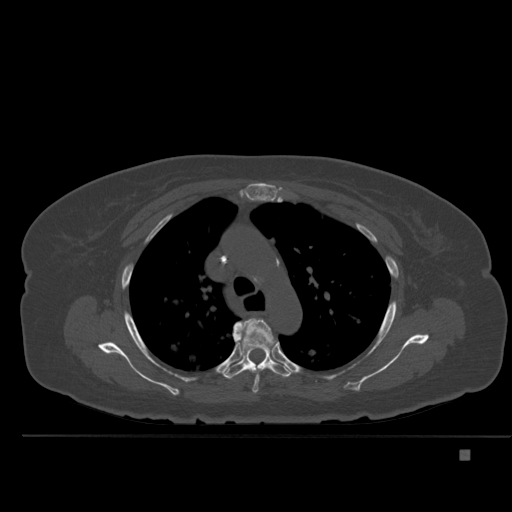
CT including the spine, one axial slice. Slice 359 of 477 in the series (ordered by position). Bone window (W 1800 / L 400 HU). 512 × 512 image matrix. Patient: female, 74 years. From the clinical record (not read from this slice): primary cancer: colon.
Outlined on this slice (semi-automatic segmentation, software-assisted and operator-edited):
- T4 vertebra: bounding box (x1, y1, x2, y2) in pixels: (235, 318, 274, 393)
- T5 vertebra: (222, 318, 293, 379)